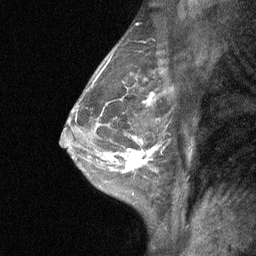
Breast MRI (dynamic contrast-enhanced), one sagittal slice; slice 41 of 64 in the series (ordered by position); dynamic contrast-enhanced study with each time point stored as its own series, time point 2 of 3 at this slice position (early post-contrast, ordered by acquisition time); 1.5 T; TE 4.8 ms, TR 27 ms; 256 × 256 image matrix, field of view 180 × 180 mm. Patient: female, 47 years. From the clinical record (not read from this slice): setting: breast cancer imaged before/during neoadjuvant chemotherapy; receptor status: HR-positive, HER2-negative.
Structures marked on this image (semi-automatic segmentation, software-assisted and operator-edited):
- analysis volume of interest (the breast-tissue region the enhancement analysis was run in; not a lesion): bounding box (x1, y1, x2, y2) in pixels: (104, 138, 161, 198)
- tumour enhancement mask (voxels above the 90 % enhancement threshold inside the analysis volume of interest): (108, 147, 155, 173)